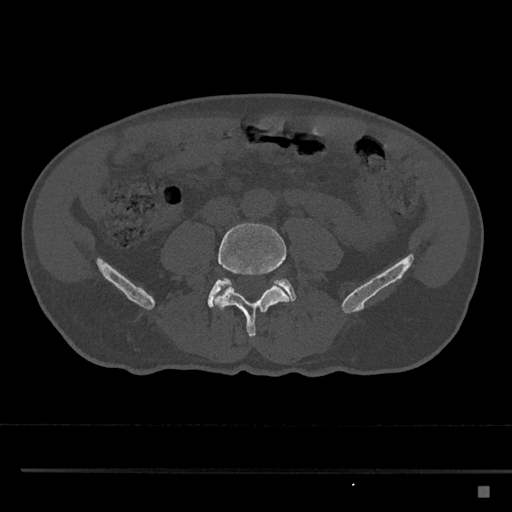
CT including the spine, one axial slice. Slice 621 of 797 in the series (ordered by position). Reconstruction kernel Br40s/3. 120 kVp. Bone window (W 1800 / L 400 HU). 0.5 mm slice thickness. 512 × 512 image matrix, field of view 391 × 391 mm. Male patient, age 59 years. From the clinical record (not read from this slice): primary cancer: prostate.
Outlined on this slice (semi-automatically segmented with operator editing):
- L4 vertebra: bounding box (x1, y1, x2, y2) in pixels: (215, 223, 291, 337)
- L5 vertebra: (208, 278, 296, 310)